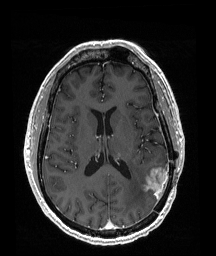
Brain MRI from a brain-tumour surgery series, one axial slice. Slice 83 of 192 in the series (ordered by position). T1-weighted post-contrast. 1 mm slice thickness. 216 × 256 image matrix, field of view 211 × 250 mm. Case-level facts recorded for this patient, not image findings: histopathology: Glioblastoma; WHO grade: 4; IDH mutation: no; tumour location: Left Temporoparietal.
Annotated regions visible in this slice (outlined manually by an expert reader):
- tumour: bounding box [x1, y1, x2, y2] px = [144, 167, 170, 196]